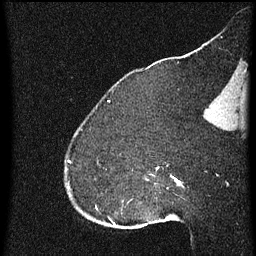
Breast MRI (dynamic contrast-enhanced), one sagittal slice. Dynamic contrast-enhanced series, image 2 of 4 at this slice position (ordered by acquisition). 1.5 T. TE 4.2 ms, TR 8 ms. 2 mm slice thickness. 256 × 256 image matrix, field of view 180 × 180 mm. Patient: female, 52 years.
Annotated regions visible in this slice (semi-automatic segmentation, software-assisted and operator-edited):
- analysis volume of interest (the breast-tissue region the enhancement analysis was run in; not a lesion): bounding box (x1, y1, x2, y2) in pixels: (73, 166, 172, 219)
- tumour enhancement mask (voxels above the 70 % enhancement threshold inside the analysis volume of interest): (157, 168, 160, 171)